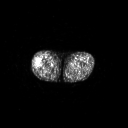
FDG PET of an extremity soft-tissue mass (from a PET/CT study), one axial slice. Position 228 of 267 along the scan axis. 128 × 128 image matrix, field of view 700 × 700 mm. Patient: male, 43 years. From the clinical record (not read from this slice): histological type: poorly differentiated synovial sarcoma; grade: high; site of the primary tumour: right buttock.
Annotated regions visible in this slice (expert contour drawn on MRI and transferred to this co-registered scan by the dataset authors):
- gross tumour volume including surrounding oedema: bounding box (x1, y1, x2, y2) in pixels: (34, 59, 43, 69)